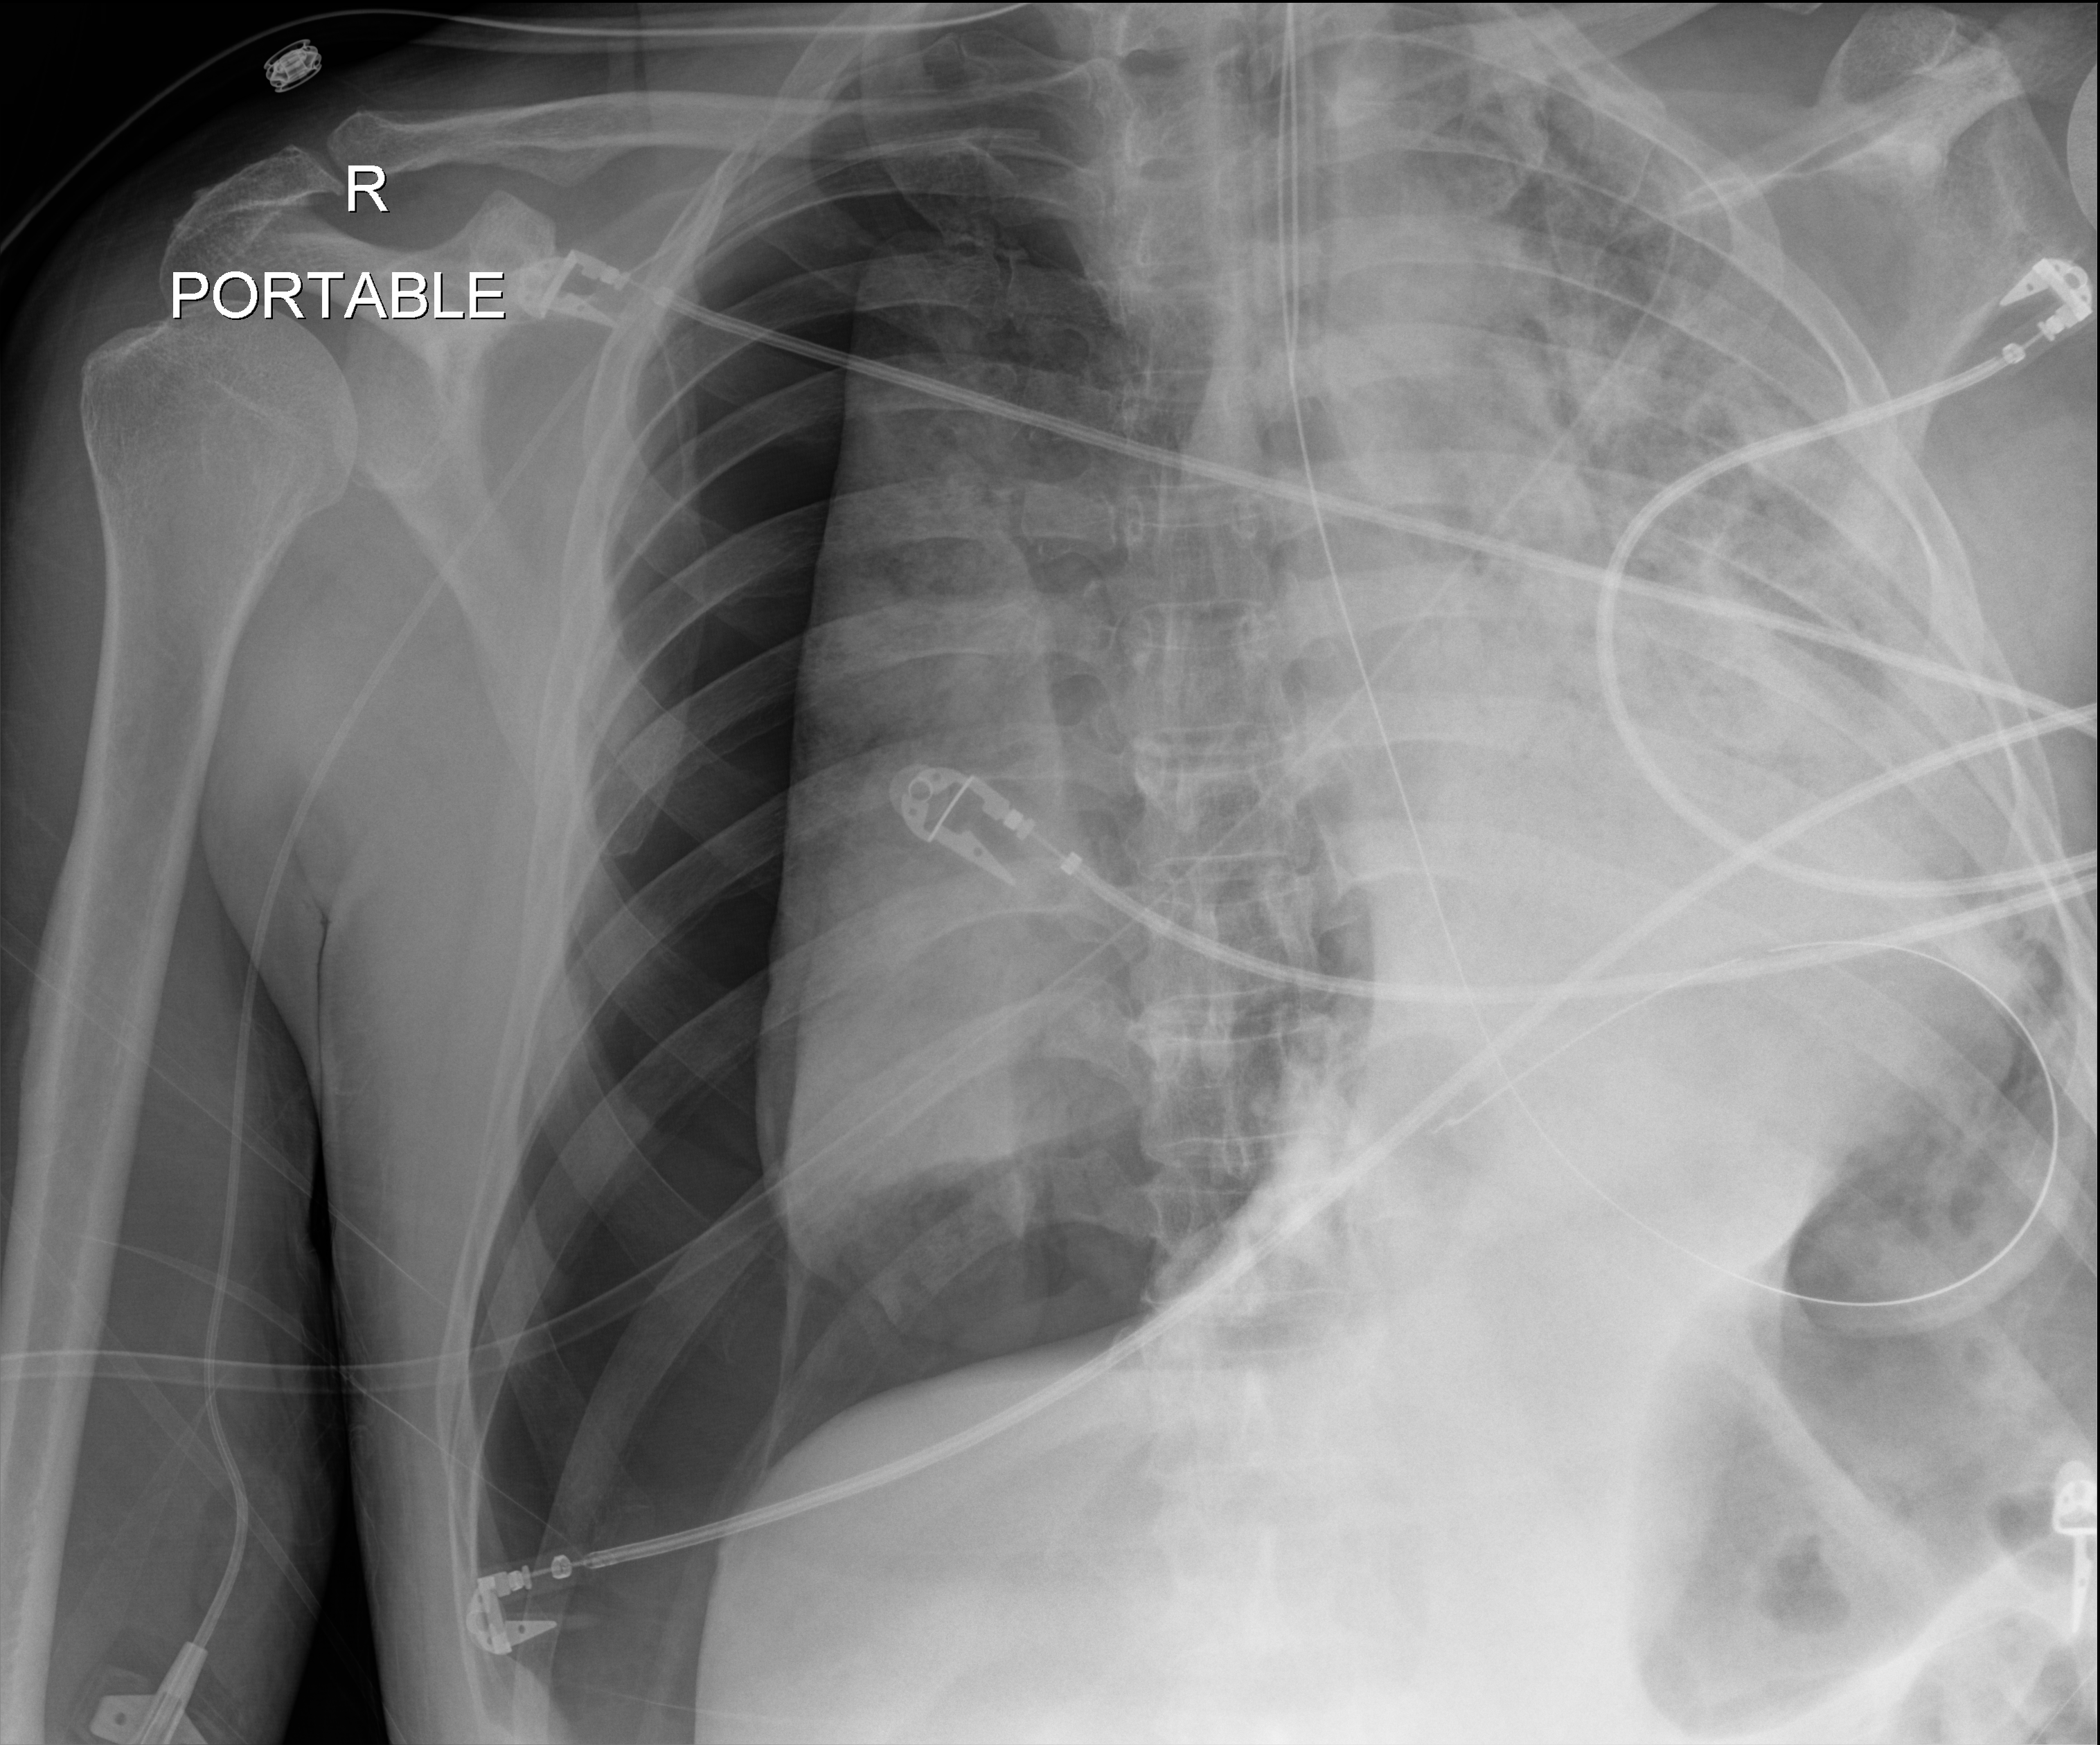
Chest radiograph, anteroposterior (AP) projection. Patient hospitalised with COVID-19; male, aged 60–74 years.
From the hospital-stay record, not from the radiograph (when in the stay this image was taken is not recorded): mechanically ventilated during this hospital stay: yes.